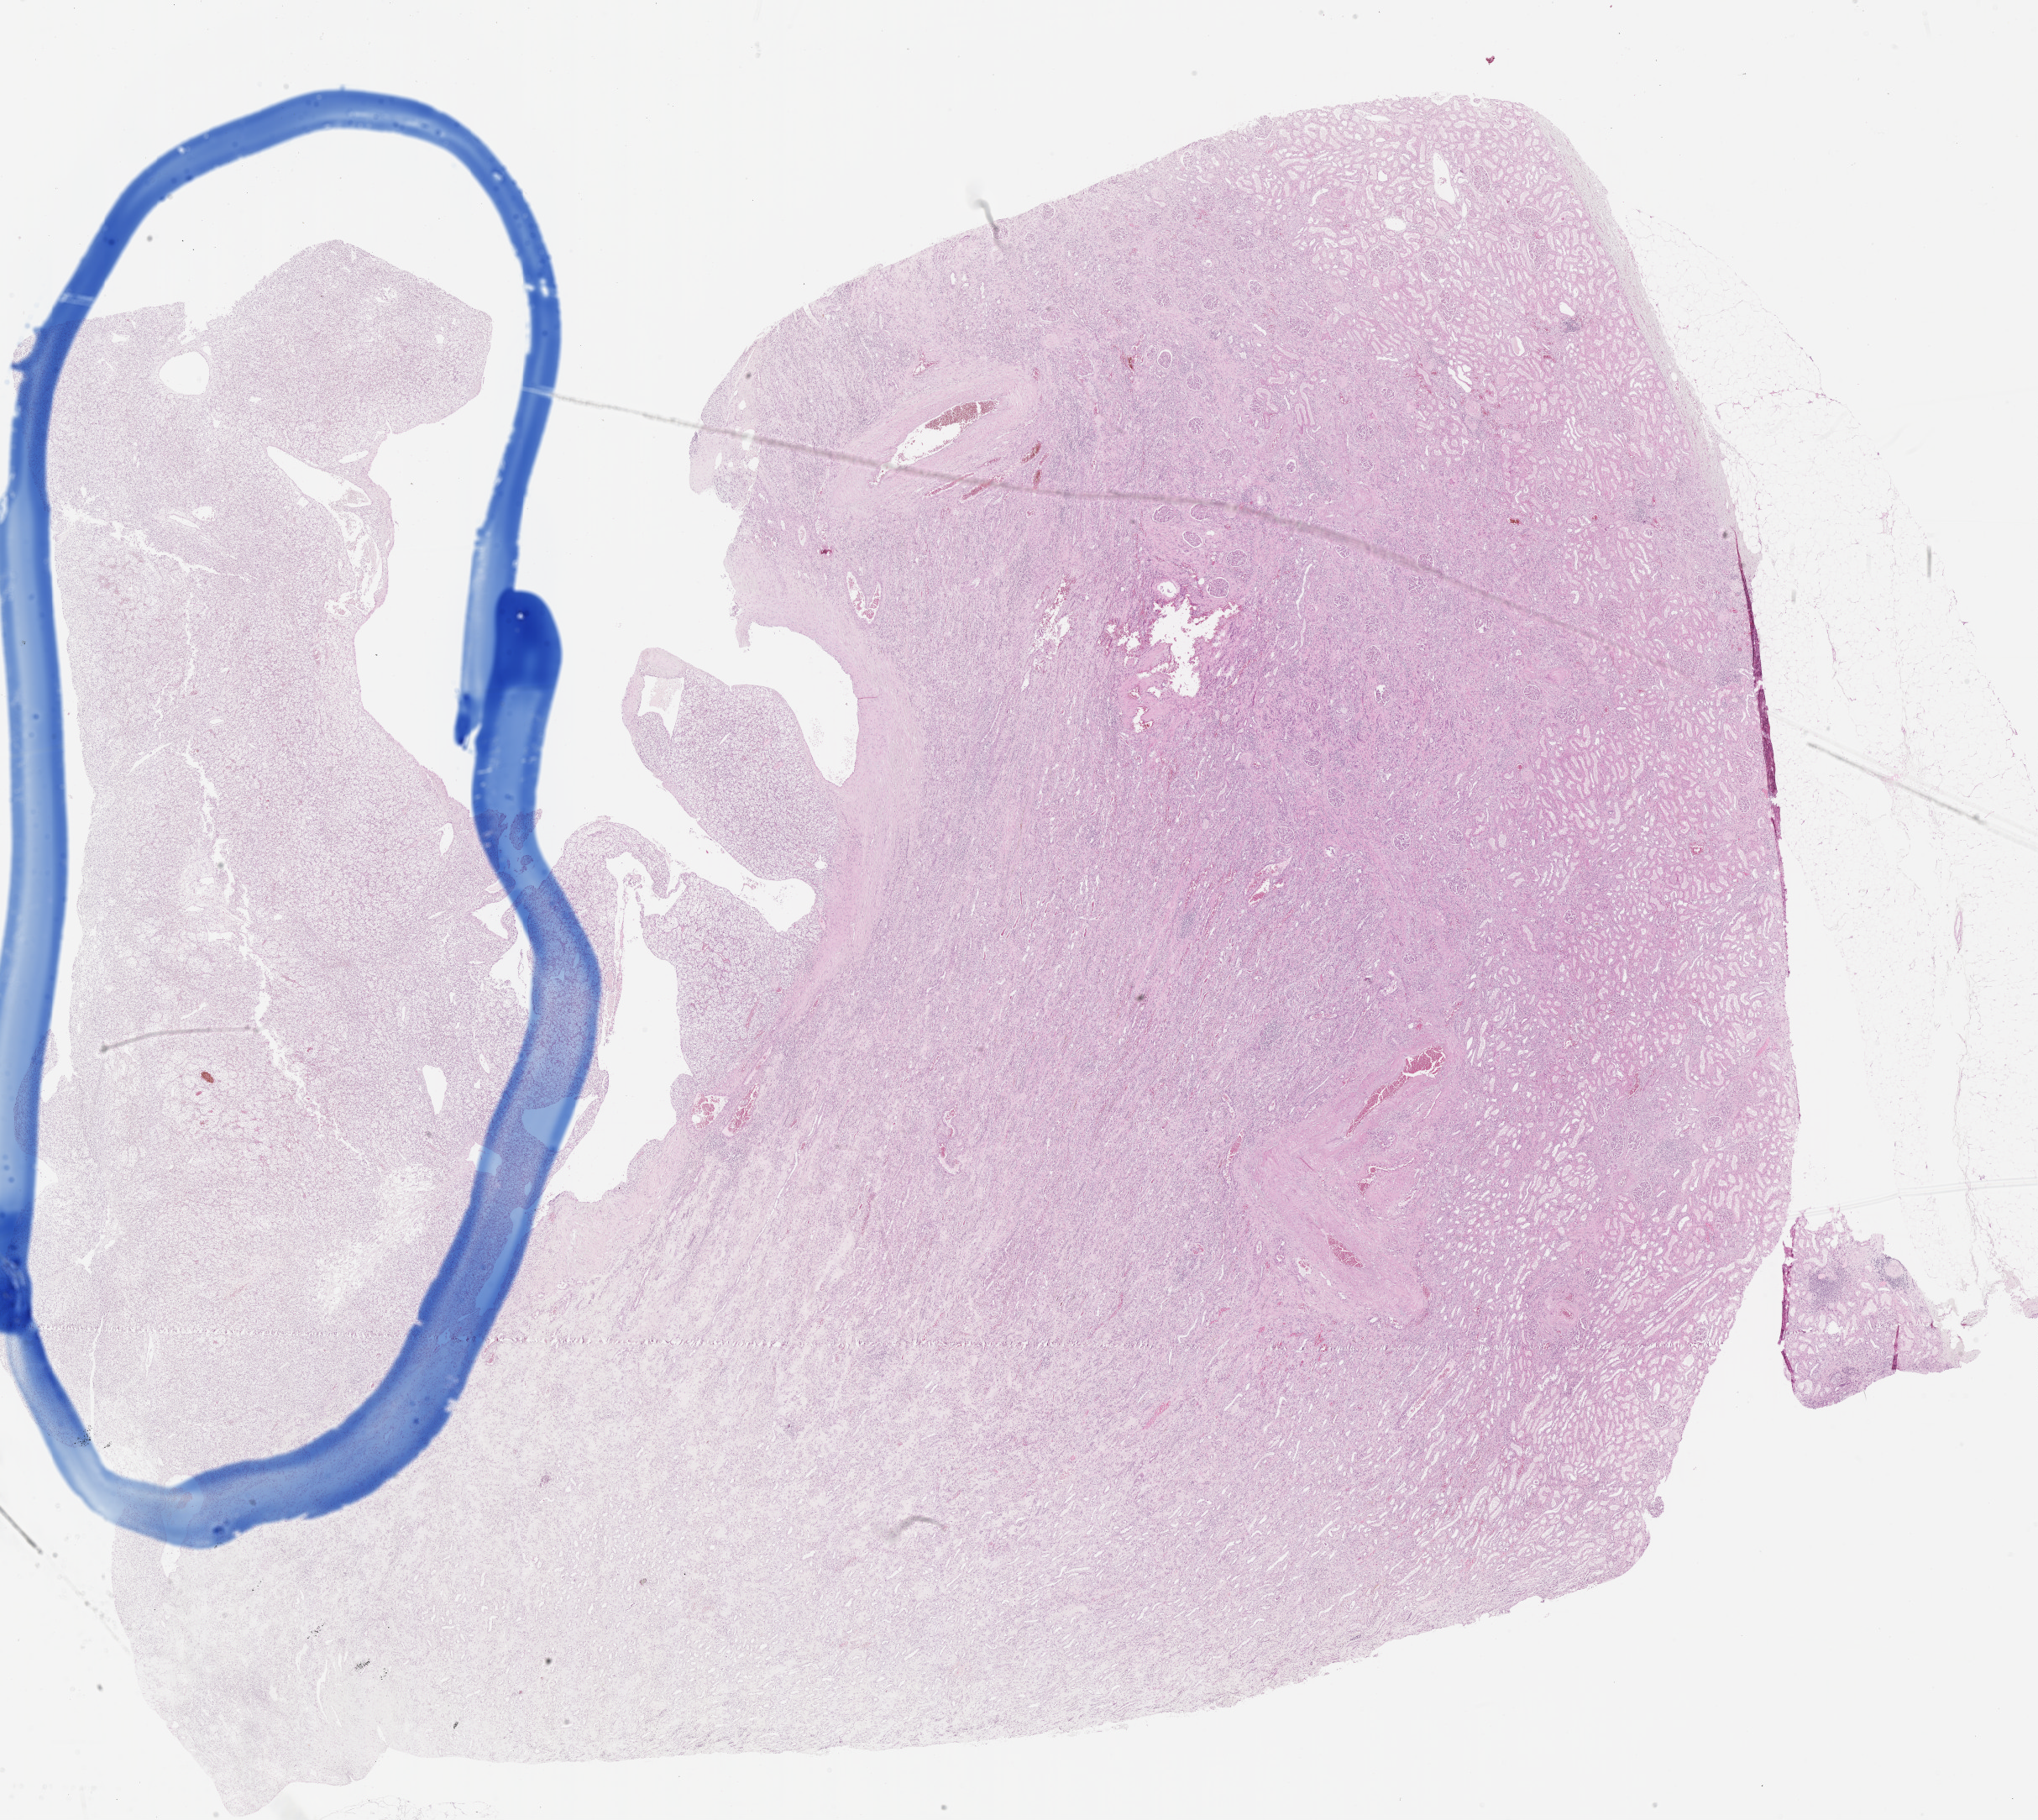
Whole-slide histology image, H&E — low-resolution overview of the scanned area, about 19.6 x 17.5 mm (acquisition: 40x scan). FFPE section. Kidney, primary tumour sample. Female patient; age at initial diagnosis 65 years. Histologic grade: G2 (moderately differentiated).
* TNM: T1b N0 M0
* AJCC pathologic stage: I
* lymph nodes positive (case pathology): 0 of 2 examined
* diagnosis: Clear cell adenocarcinoma, NOS